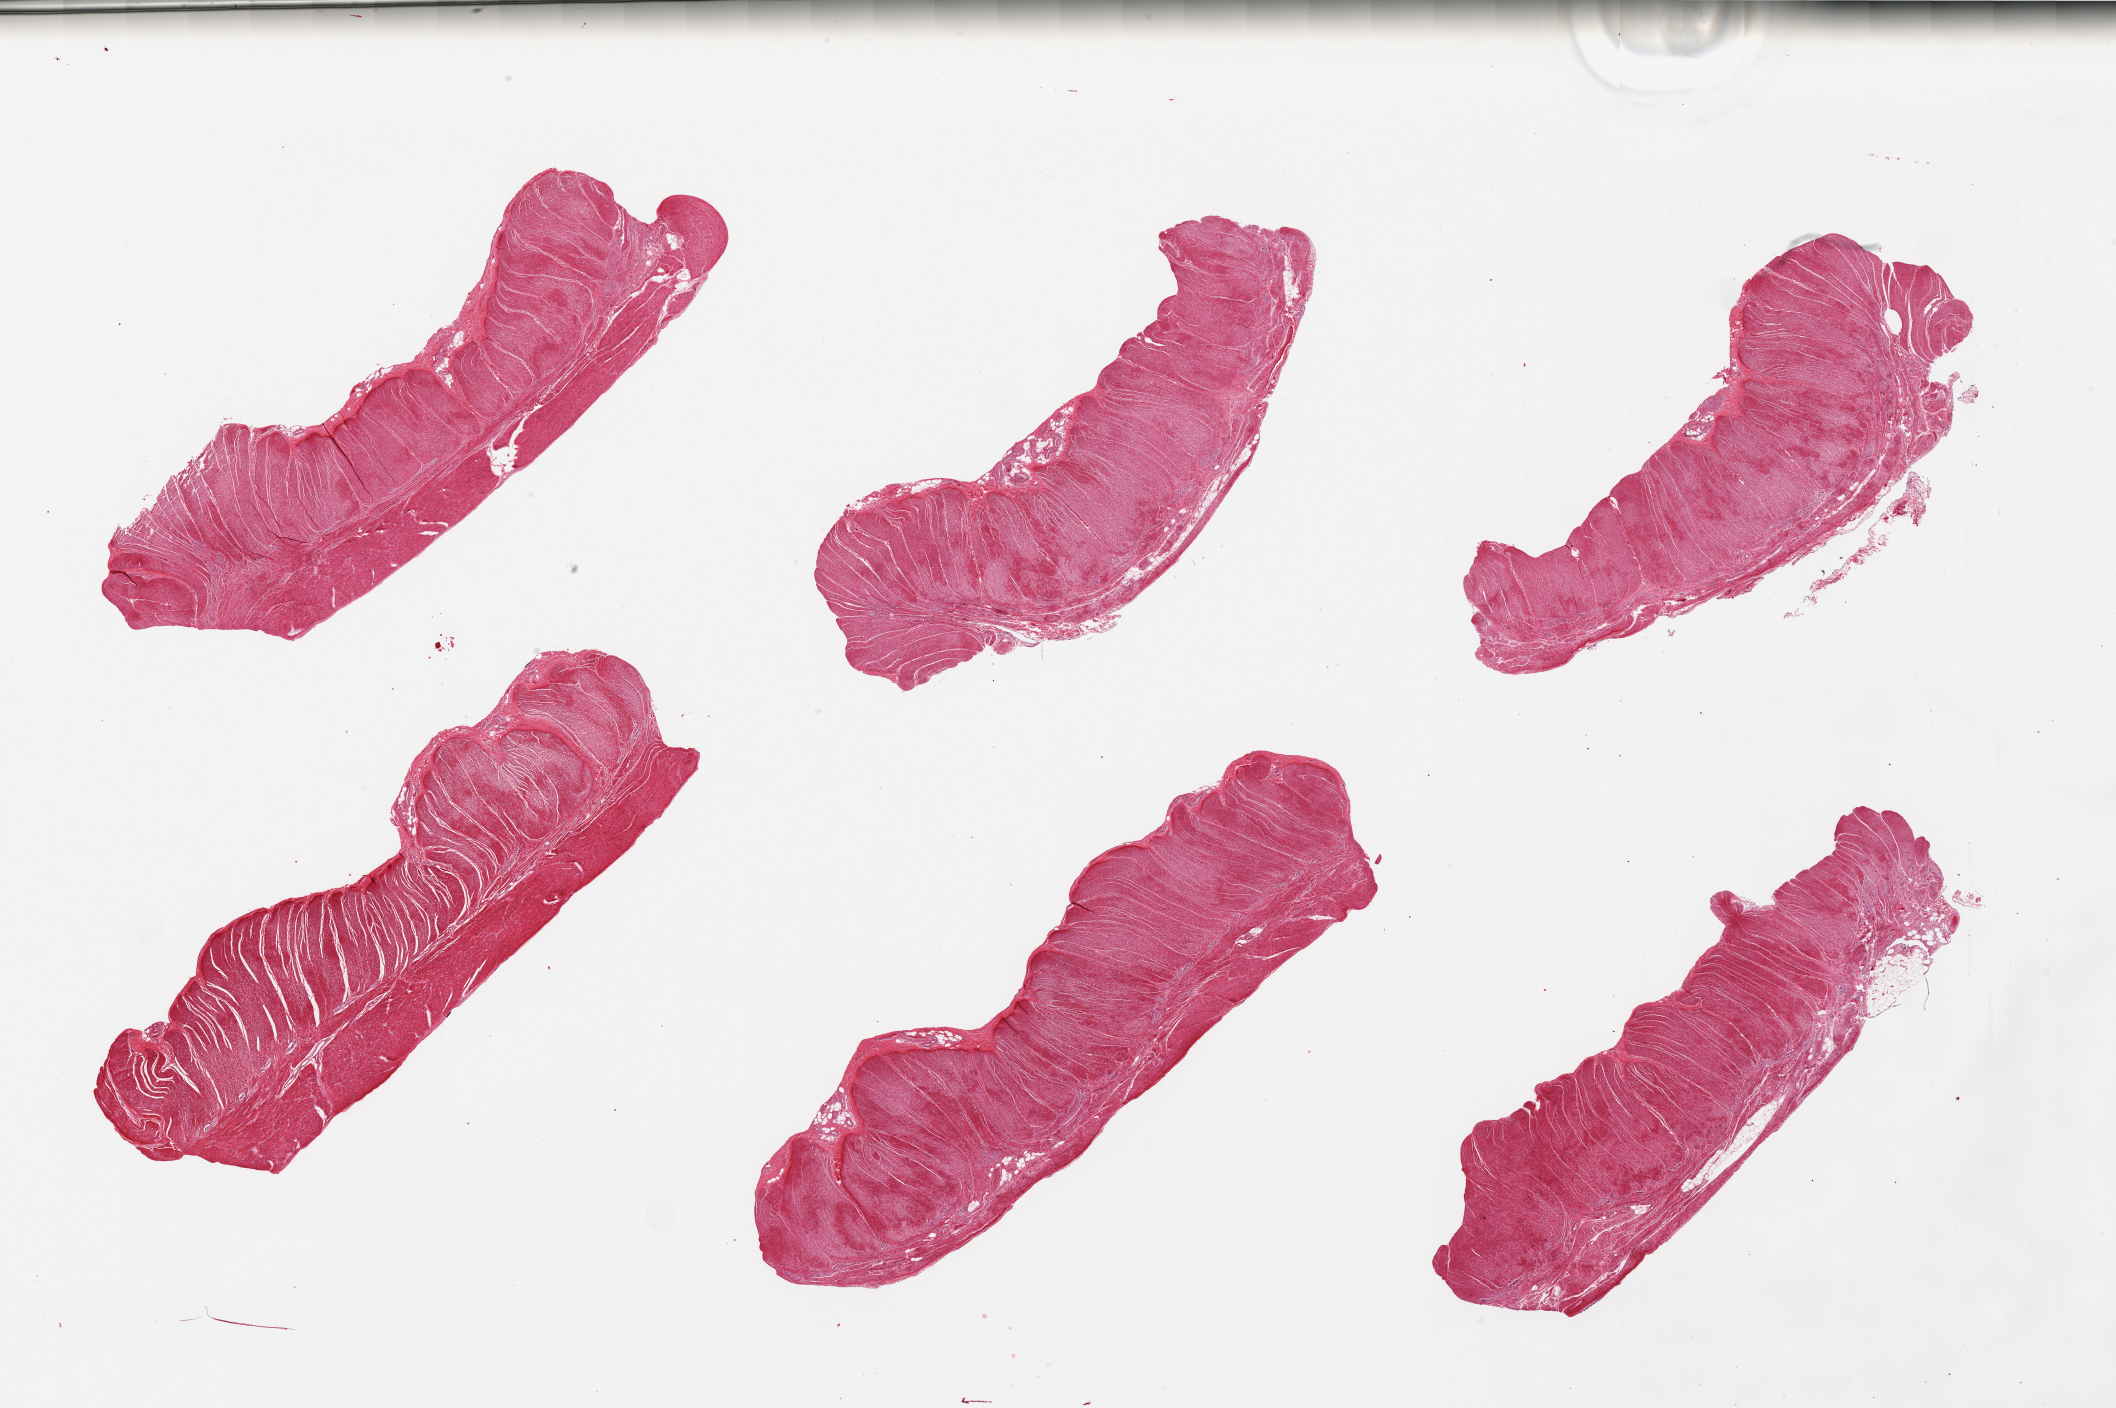
H&E whole-slide image, brightfield, a low-resolution overview of the entire scanned area, about 33.5 x 22.3 mm, PAXgene-fixed paraffin-embedded (PFPE) section, section of sigmoid colon (target tissue), tissue donor sample.
* reviewer comment on this tissue sample: 6 pieces, all muscularis, variably congested with foci of moderate autolysis